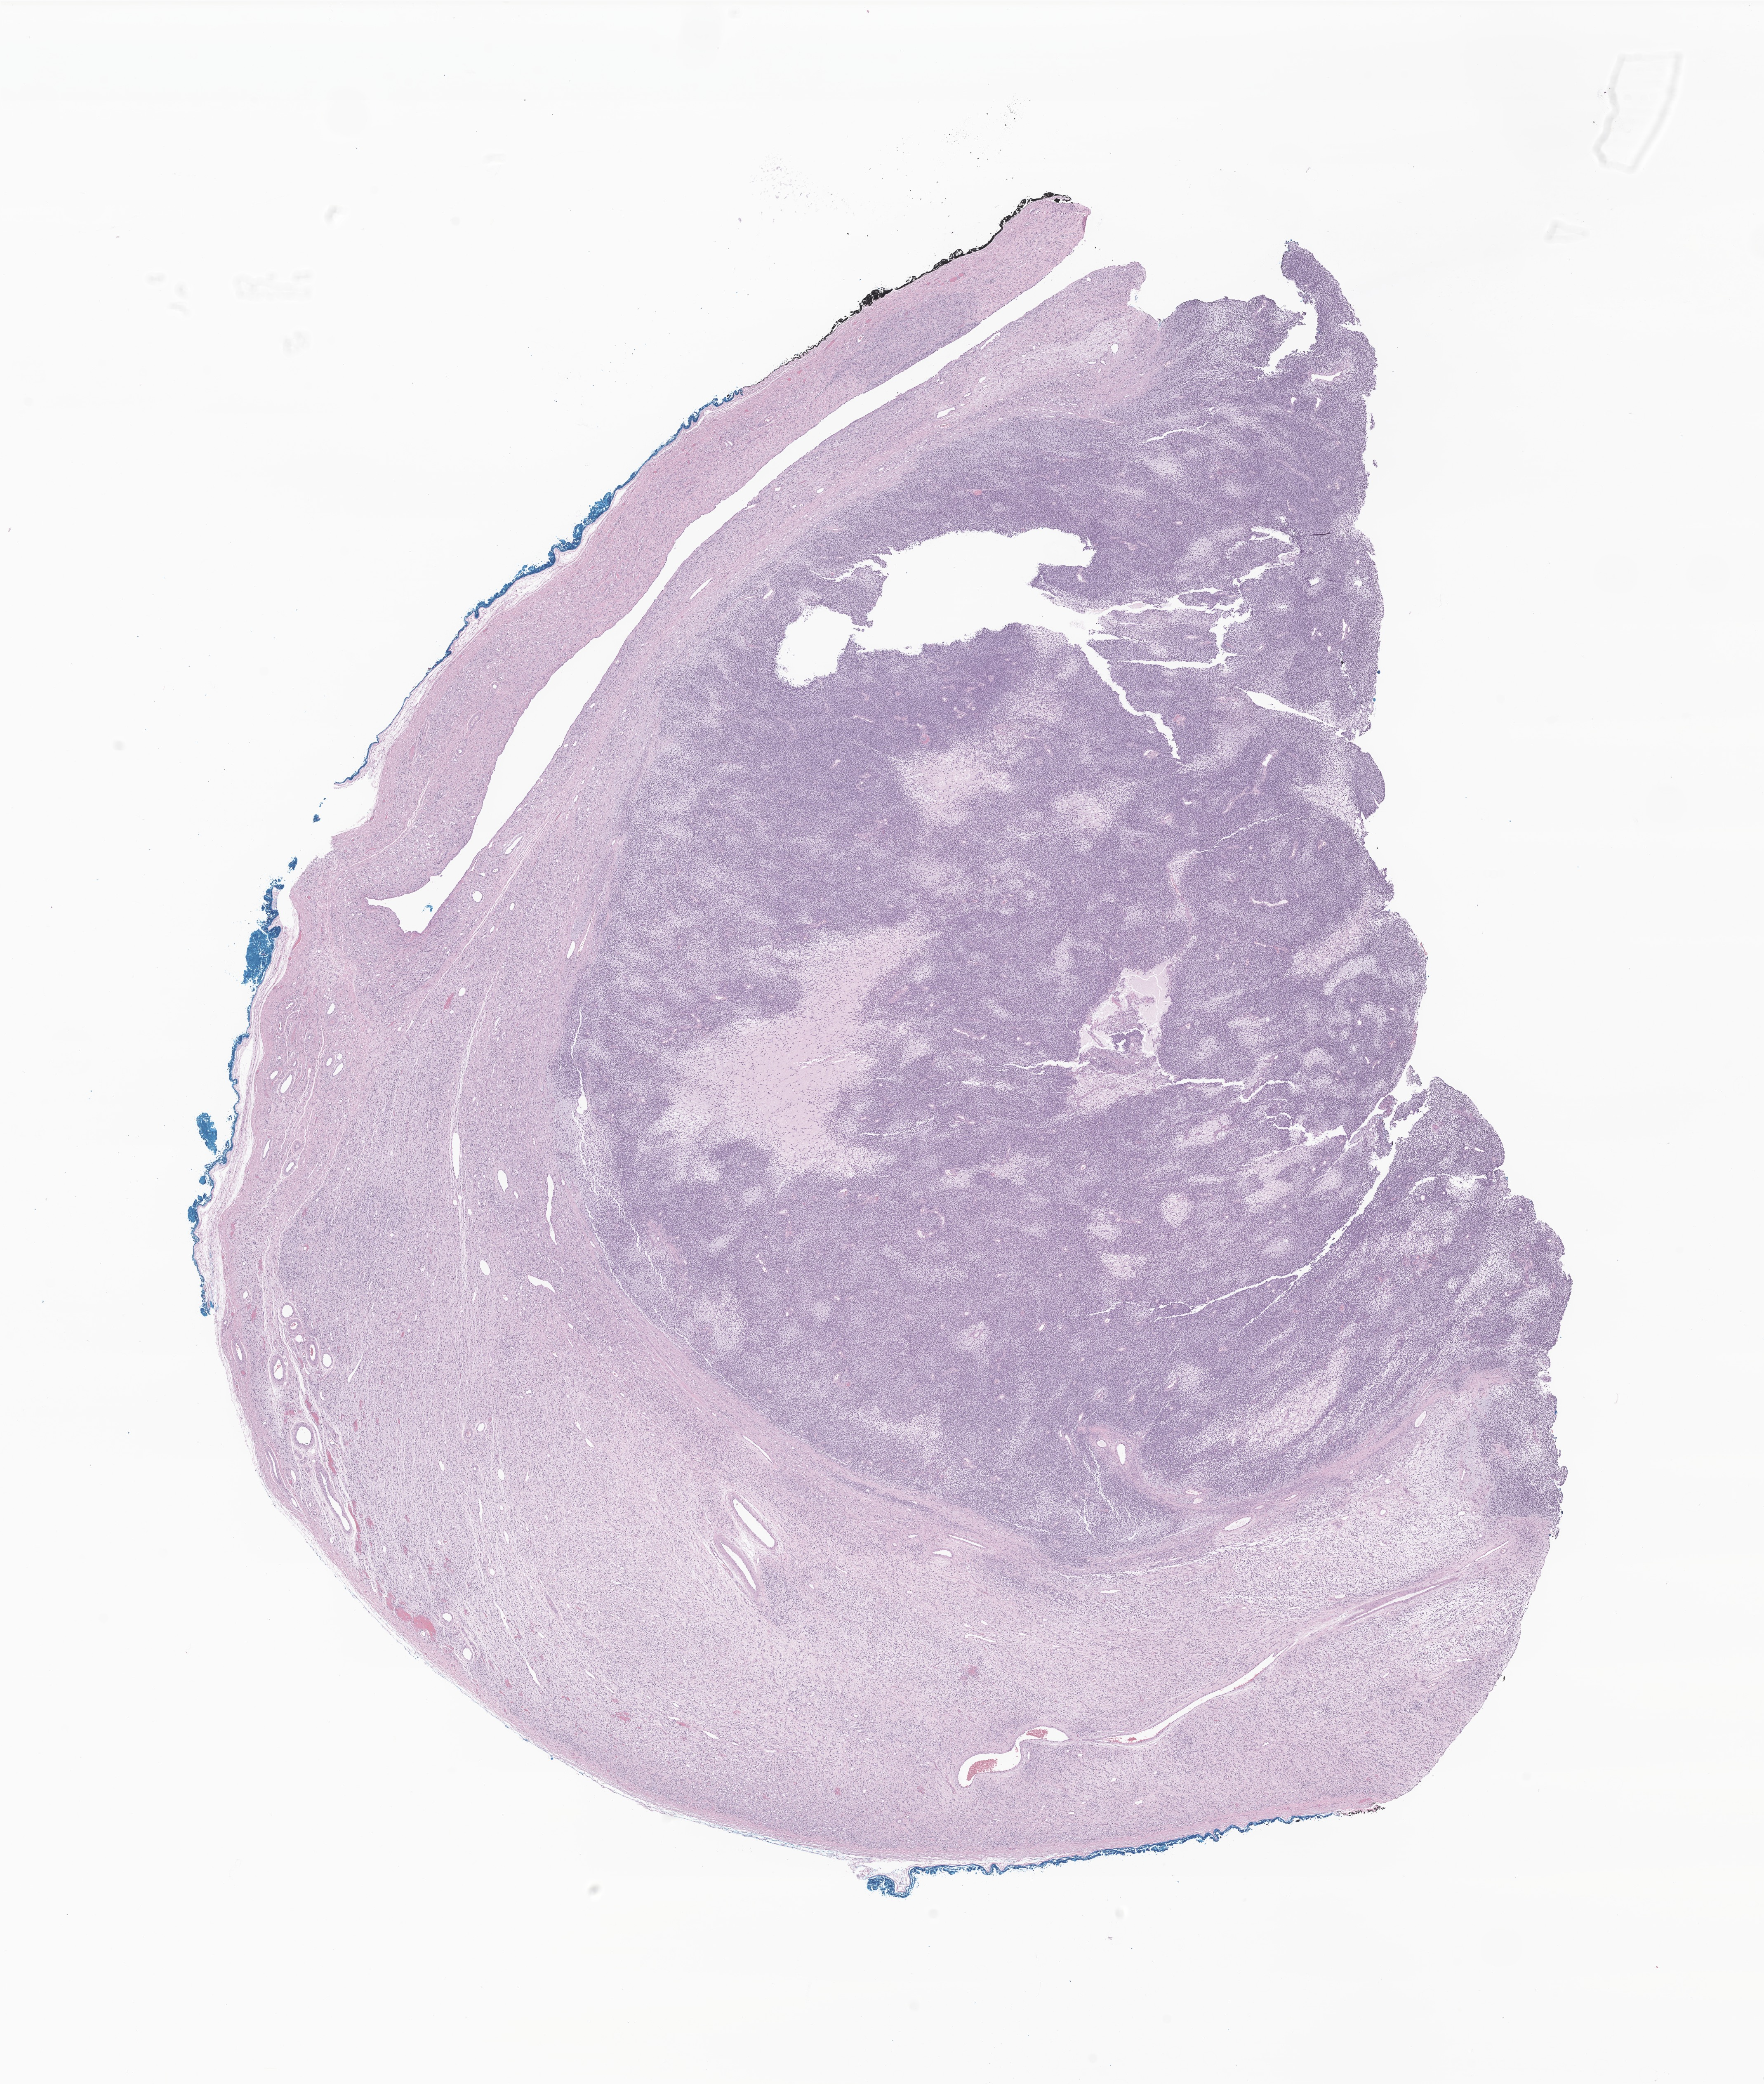
Digitized H&E-stained section of tumor tissue from the testis — low-resolution overview of the scanned area, about 18.0 x 21.3 mm; FFPE section. Patient male; age 46 months.
• recorded diagnosis: Embryonal rhabdomyosarcoma, NOS